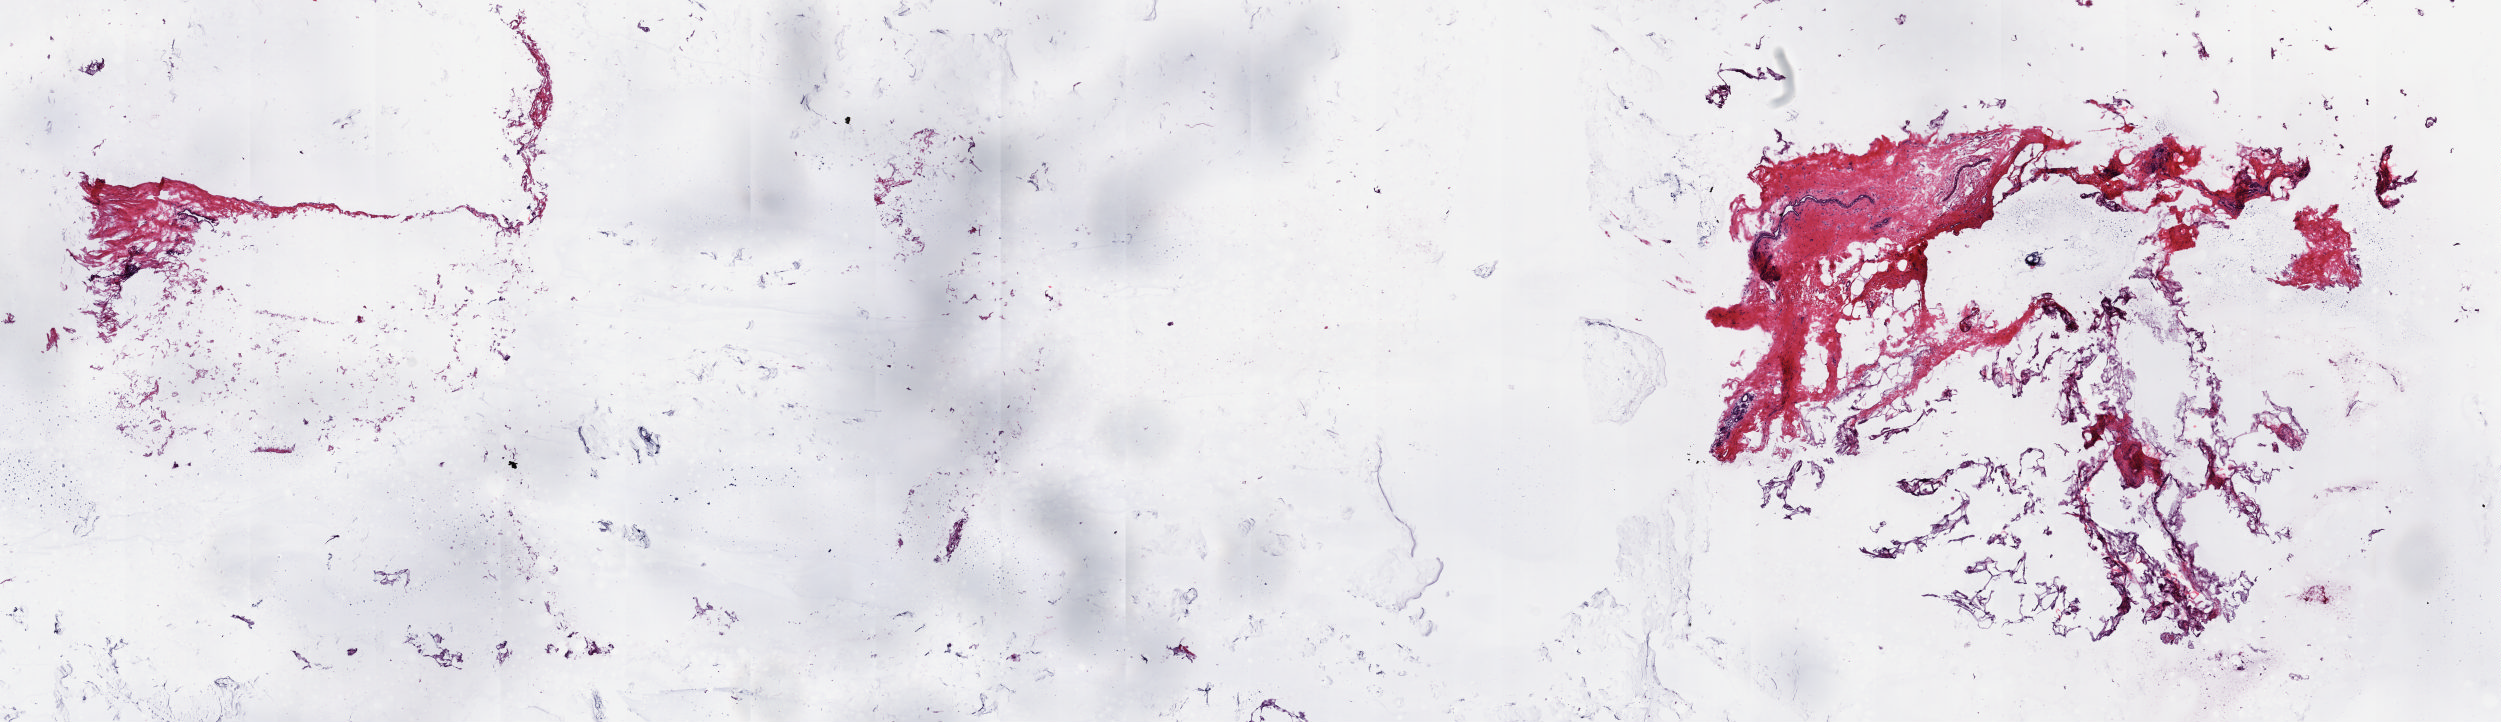
Digitized Hematoxylin and eosin (H&E) stained tissue section (whole slide), a low-resolution overview of the entire scanned area, about 19.8 x 5.7 mm (acquisition: 20x scan); frozen section; breast, solid tissue normal (non-tumour tissue) sample. Female patient; age at initial diagnosis 44 years. Composition of this section per pathologist review: tumour cells 0%, tumour nuclei 0%, normal cells 100%, stromal cells 0%, necrosis 0%. Inflammatory infiltration, as recorded: lymphocyte infiltration 0%, monocyte infiltration 0%, neutrophil infiltration 0%.
• this section: solid tissue normal (non-tumour) sample from the same patient
• patient diagnosis: Infiltrating duct carcinoma, NOS